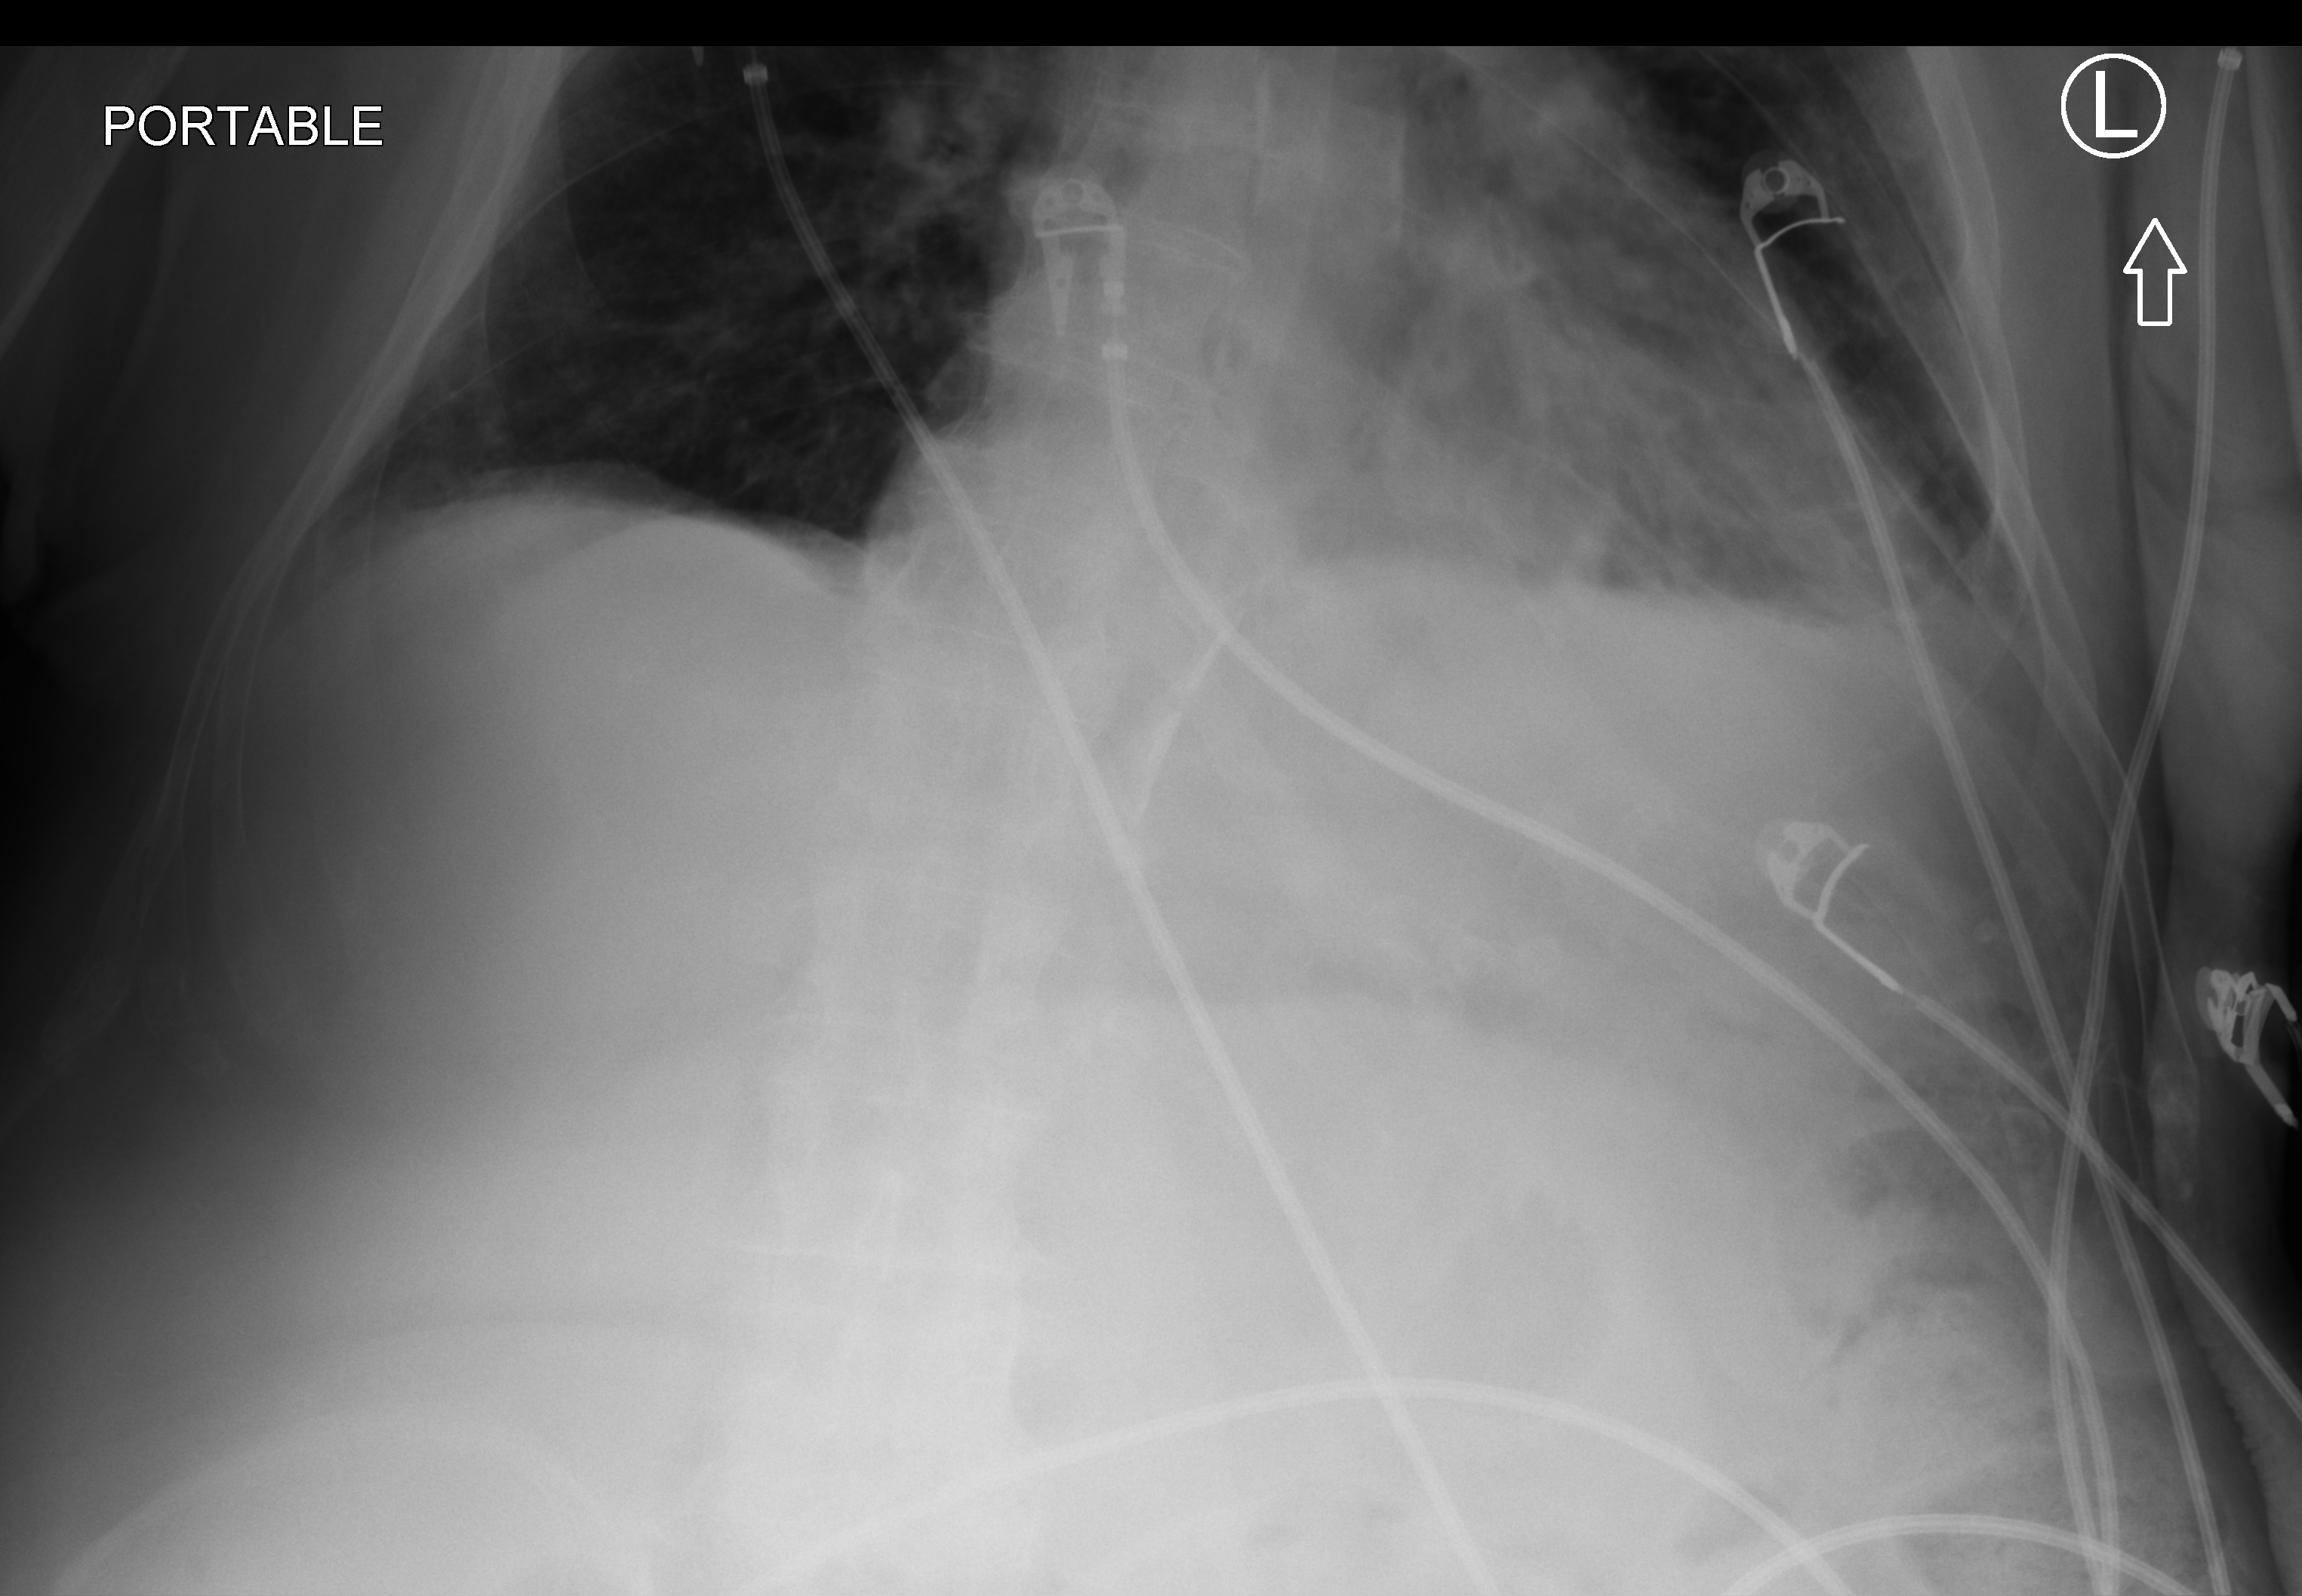
Portable abdomen radiograph. Patient hospitalised with COVID-19; male, aged 75–90 years.
Admission-level facts for this patient (not findings on this image; timing relative to this image not recorded):
- admitted to intensive care during this hospital stay: no
- COPD (admission record): no